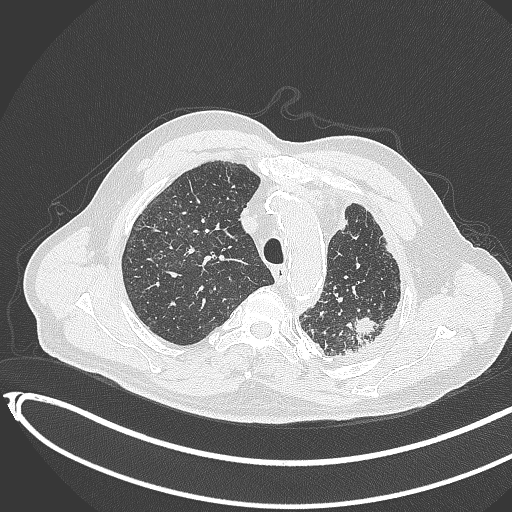
Chest CT, one axial slice; slice 338 of 451 in the series (ordered by position); lung window (W 1500 / L -600 HU); 512 × 512 image matrix, field of view 400 × 400 mm. Patient: male, 78 years. From the clinical record (not read from this slice): clinical TNM (as recorded): T1c N0 M1.
Annotated regions visible in this slice (rectangle marked by the reading radiologist):
- lung tumour (recorded histology: adenocarcinoma): bounding box <348,311,383,343> (left, top, right, bottom; pixels)